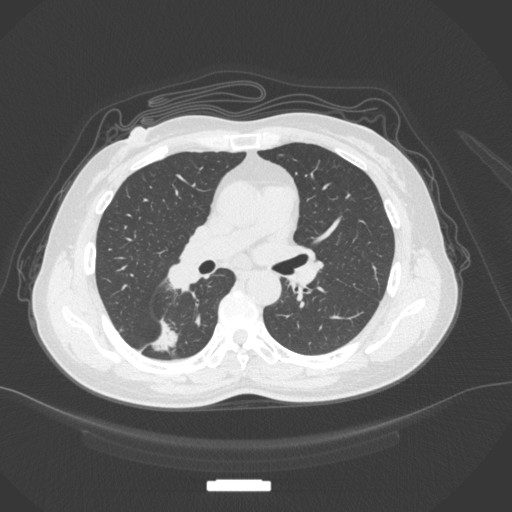
Chest CT, one axial slice. Reconstruction kernel B31f. 120 kVp. Lung window (W 1500 / L -600 HU). 1 mm slice thickness. 512 × 512 image matrix, field of view 400 × 400 mm. Patient: female, 55 years. Case-level facts recorded for this patient, not image findings: clinical TNM (as recorded): T1c N1 M0.
Annotated regions visible in this slice (rectangle marked by the reading radiologist):
- lung tumour (recorded histology: adenocarcinoma): bounding box [x1, y1, x2, y2] px = [148, 318, 184, 361]